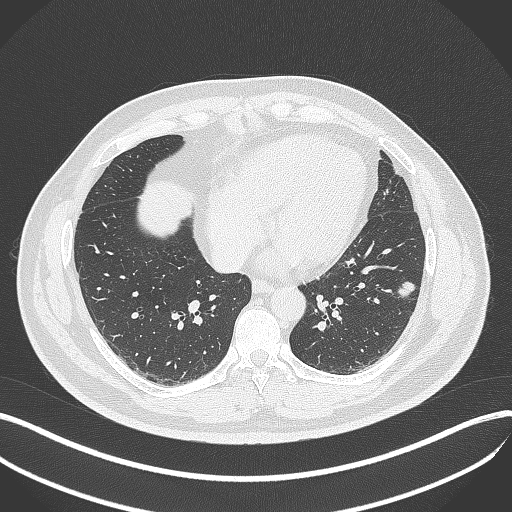
Chest CT, one axial slice; position 153 of 429 along the scan axis; 120 kVp; lung window (W 1500 / L -600 HU); 512 × 512 image matrix, field of view 400 × 400 mm. Male patient, age 39 years. From the clinical record (not read from this slice): clinical TNM (as recorded): T2a N0 M0; histopathological grade: G2-3.
Outlined on this slice (bounding box drawn by a radiologist):
- lung tumour (recorded histology: adenocarcinoma): bounding box <395,278,416,303> (left, top, right, bottom; pixels)